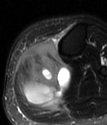
MRI of an extremity soft-tissue mass, one axial slice. Slice 31 of 78 in the series (ordered by position). T2-weighted fat-saturated. MR volume resampled by the dataset authors to the PET/CT grid (not the native acquisition matrix). 3.27 mm slice thickness. 107 × 125 image matrix. Female patient. From the clinical record (not read from this slice): histological type: extraskeletal high grade osteogenic sarcoma; grade: high; site of the primary tumour: left calf.
Outlined on this slice (expert contour drawn on MRI and transferred to this co-registered scan by the dataset authors):
- gross tumour volume (mass): bounding box (x1, y1, x2, y2) in pixels: (17, 40, 70, 108)